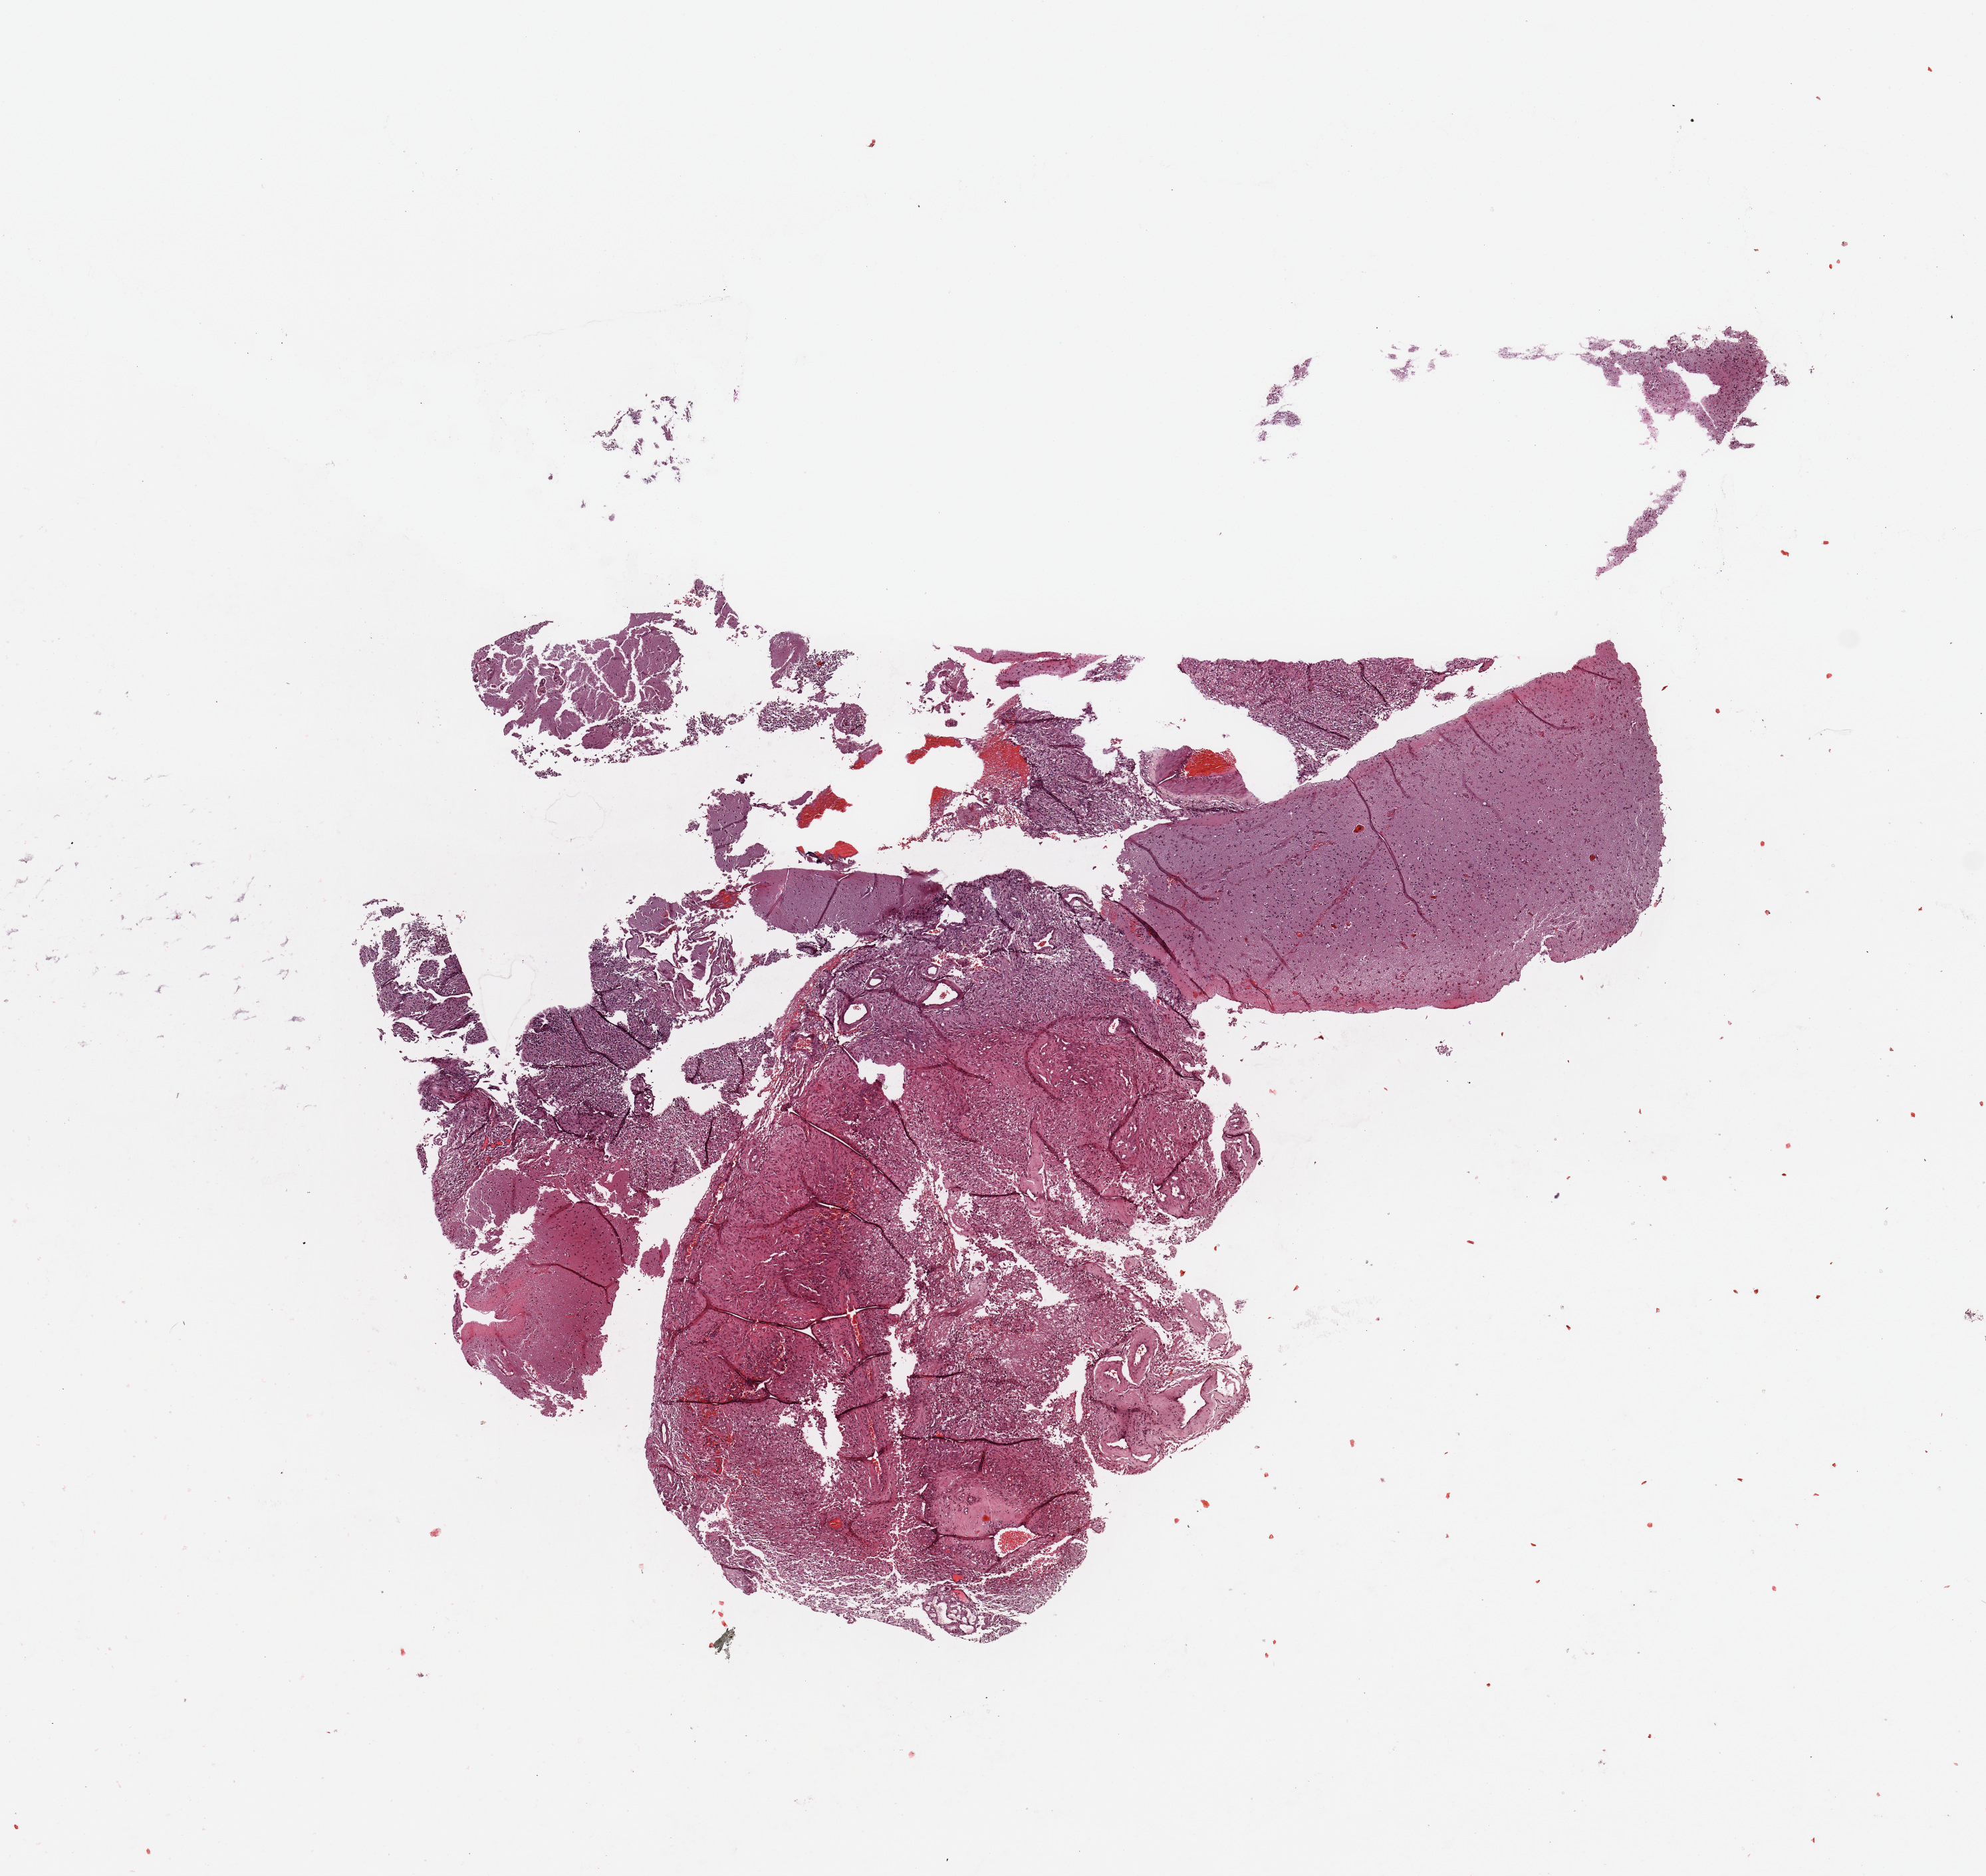
Whole-slide histology image, H&E, shown as a low-resolution overview of the whole scanned area (about 11.8 x 11.2 mm, from a 20x scan). Brain, tumour tissue. Patient: male, age 59 years.
Histologic diagnosis: Glioblastoma.